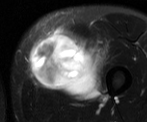
MRI of an extremity soft-tissue mass, one axial slice; slice 20 of 52 in the series (ordered by position); T2-weighted fat-saturated; MR volume resampled by the dataset authors to the PET/CT grid (not the native acquisition matrix); 3.27 mm slice thickness; 147 × 122 image matrix. Male patient. From the clinical record (not read from this slice): histological type: pleiomorphic liposarcoma; grade: high; site of the primary tumour: left thigh.
Outlined on this slice (expert contour drawn on MRI and transferred to this co-registered scan by the dataset authors):
- gross tumour volume including surrounding oedema: bounding box (x1, y1, x2, y2) in pixels: (28, 21, 108, 102)
- gross tumour volume (mass): (28, 32, 99, 97)